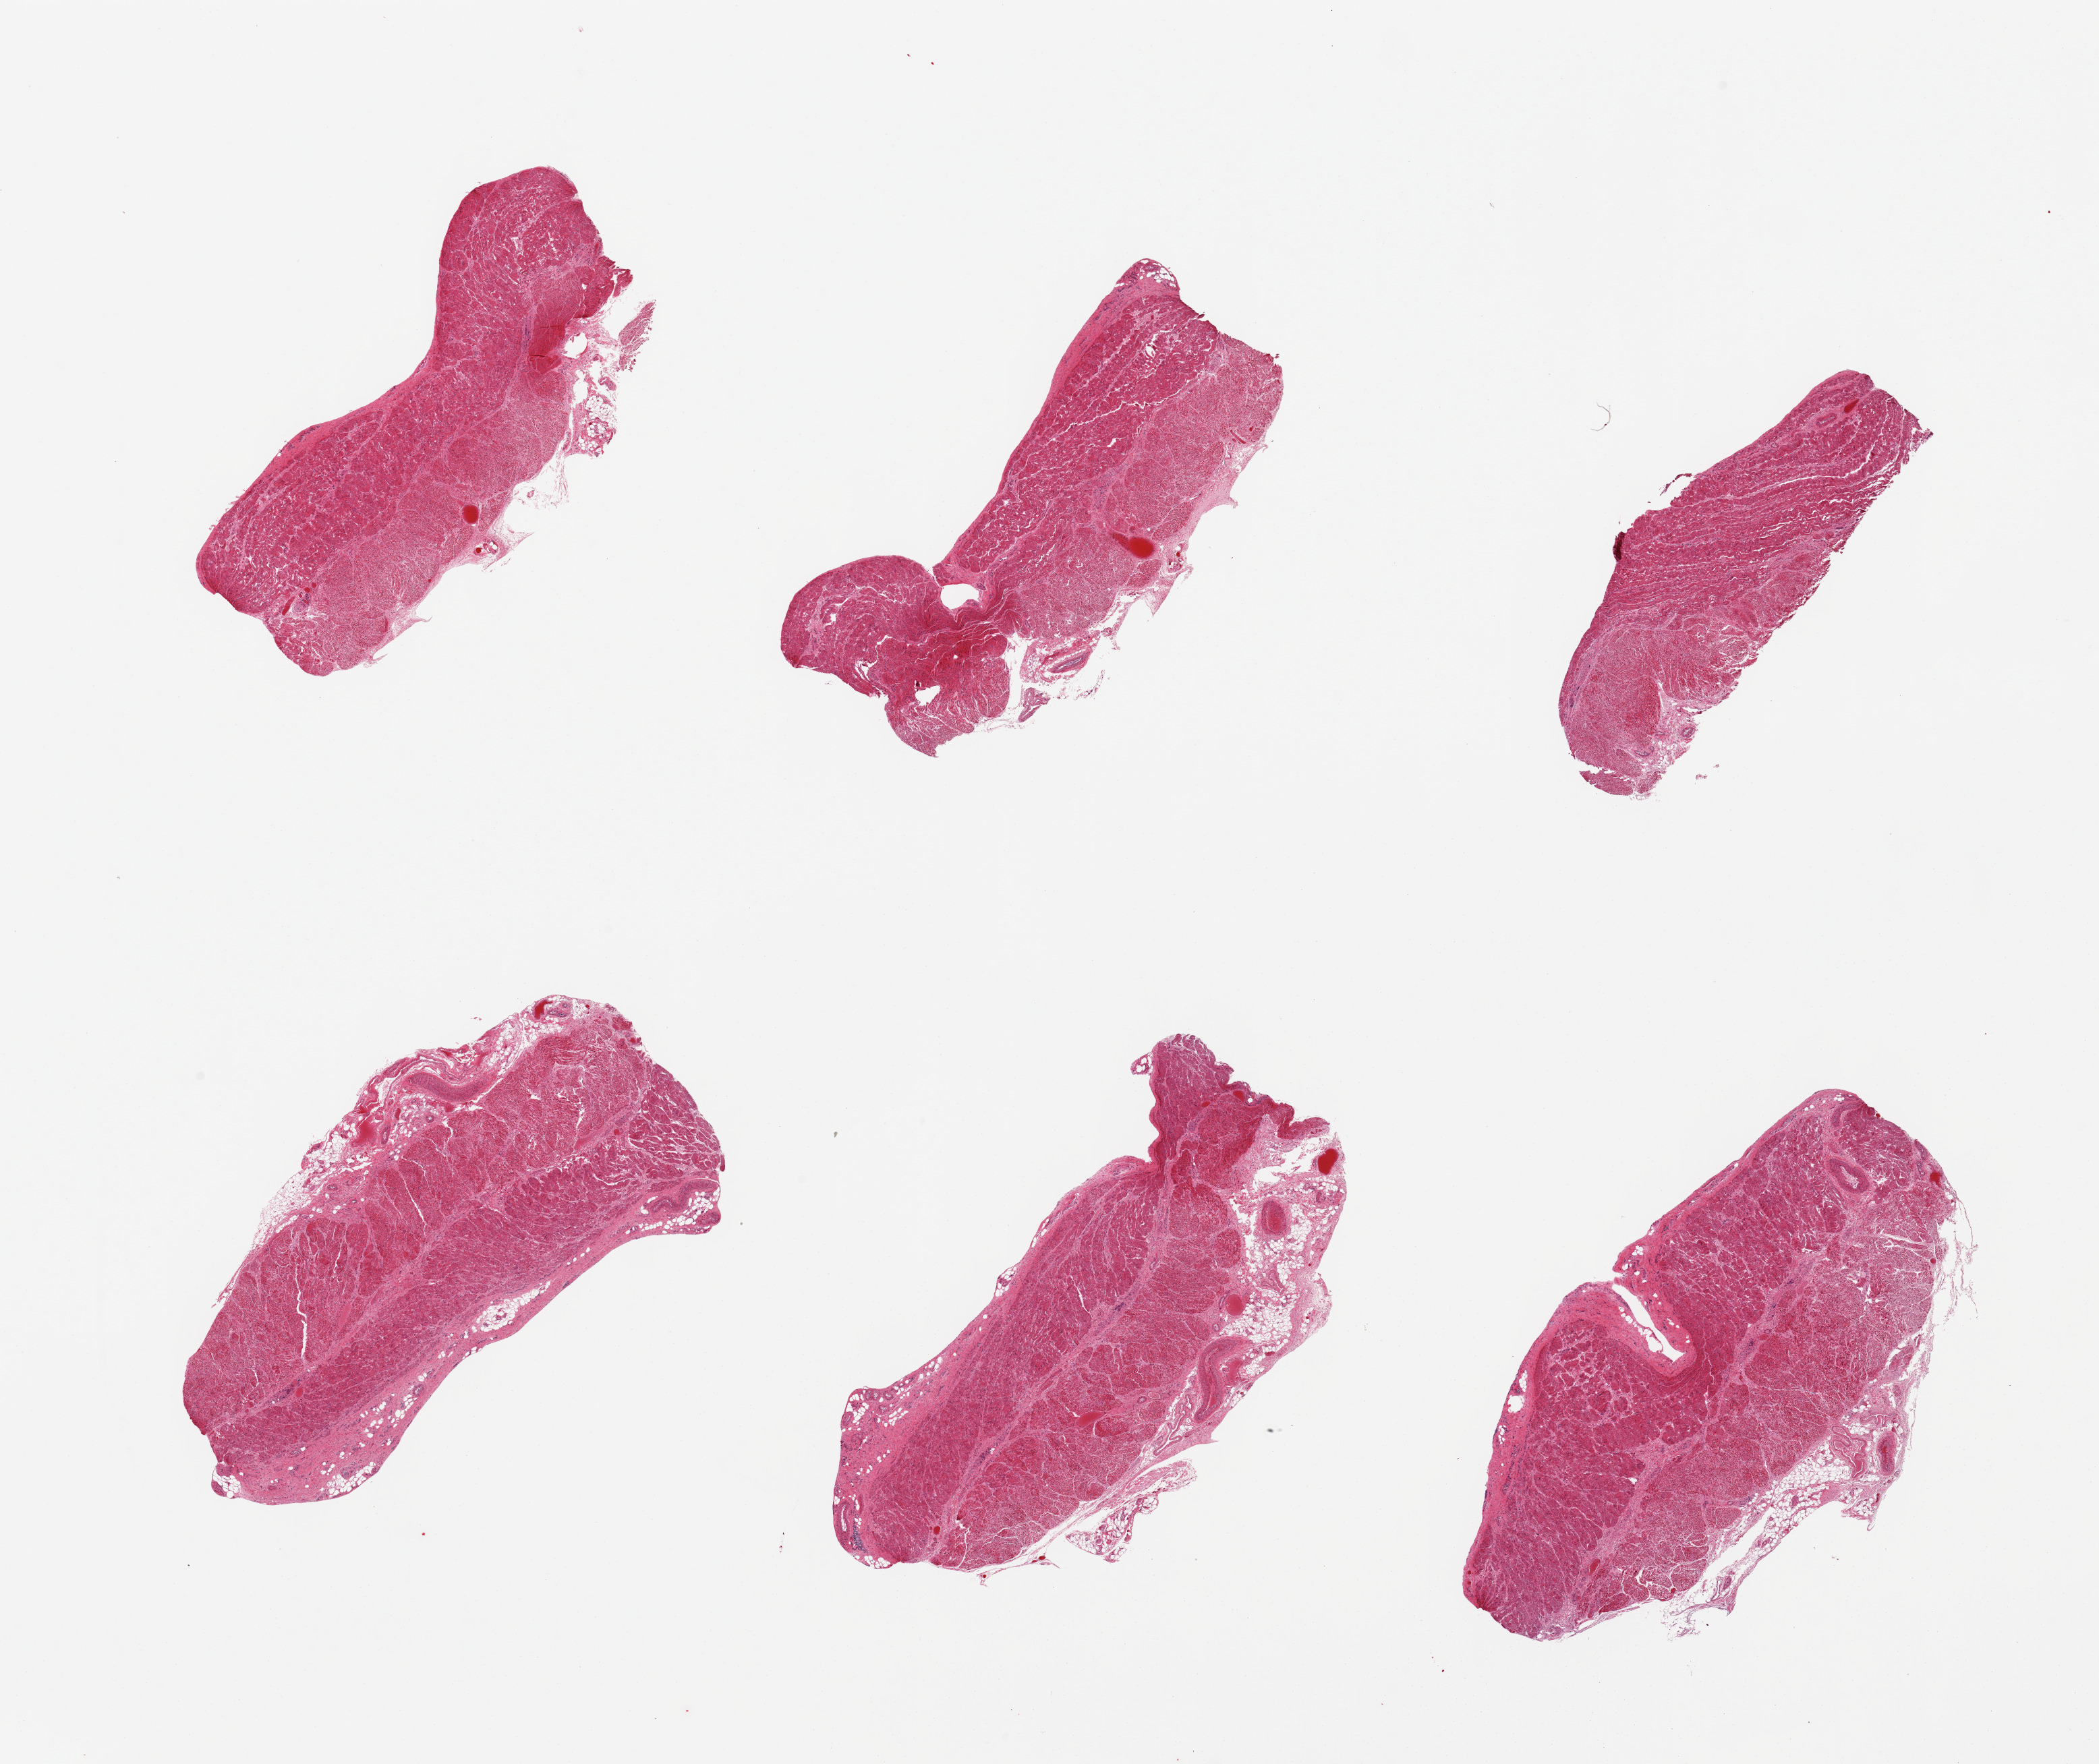
Digitized hematoxylin and eosin (H&E)-stained section — shown as a low-resolution overview of the whole scanned area (about 24.6 x 20.7 mm), PAXgene-fixed, paraffin-embedded tissue, sampled site (target tissue): gastroesophageal junction, tissue donor sample. Male donor.
- review note (as recorded): 6 pieces; well trimmed